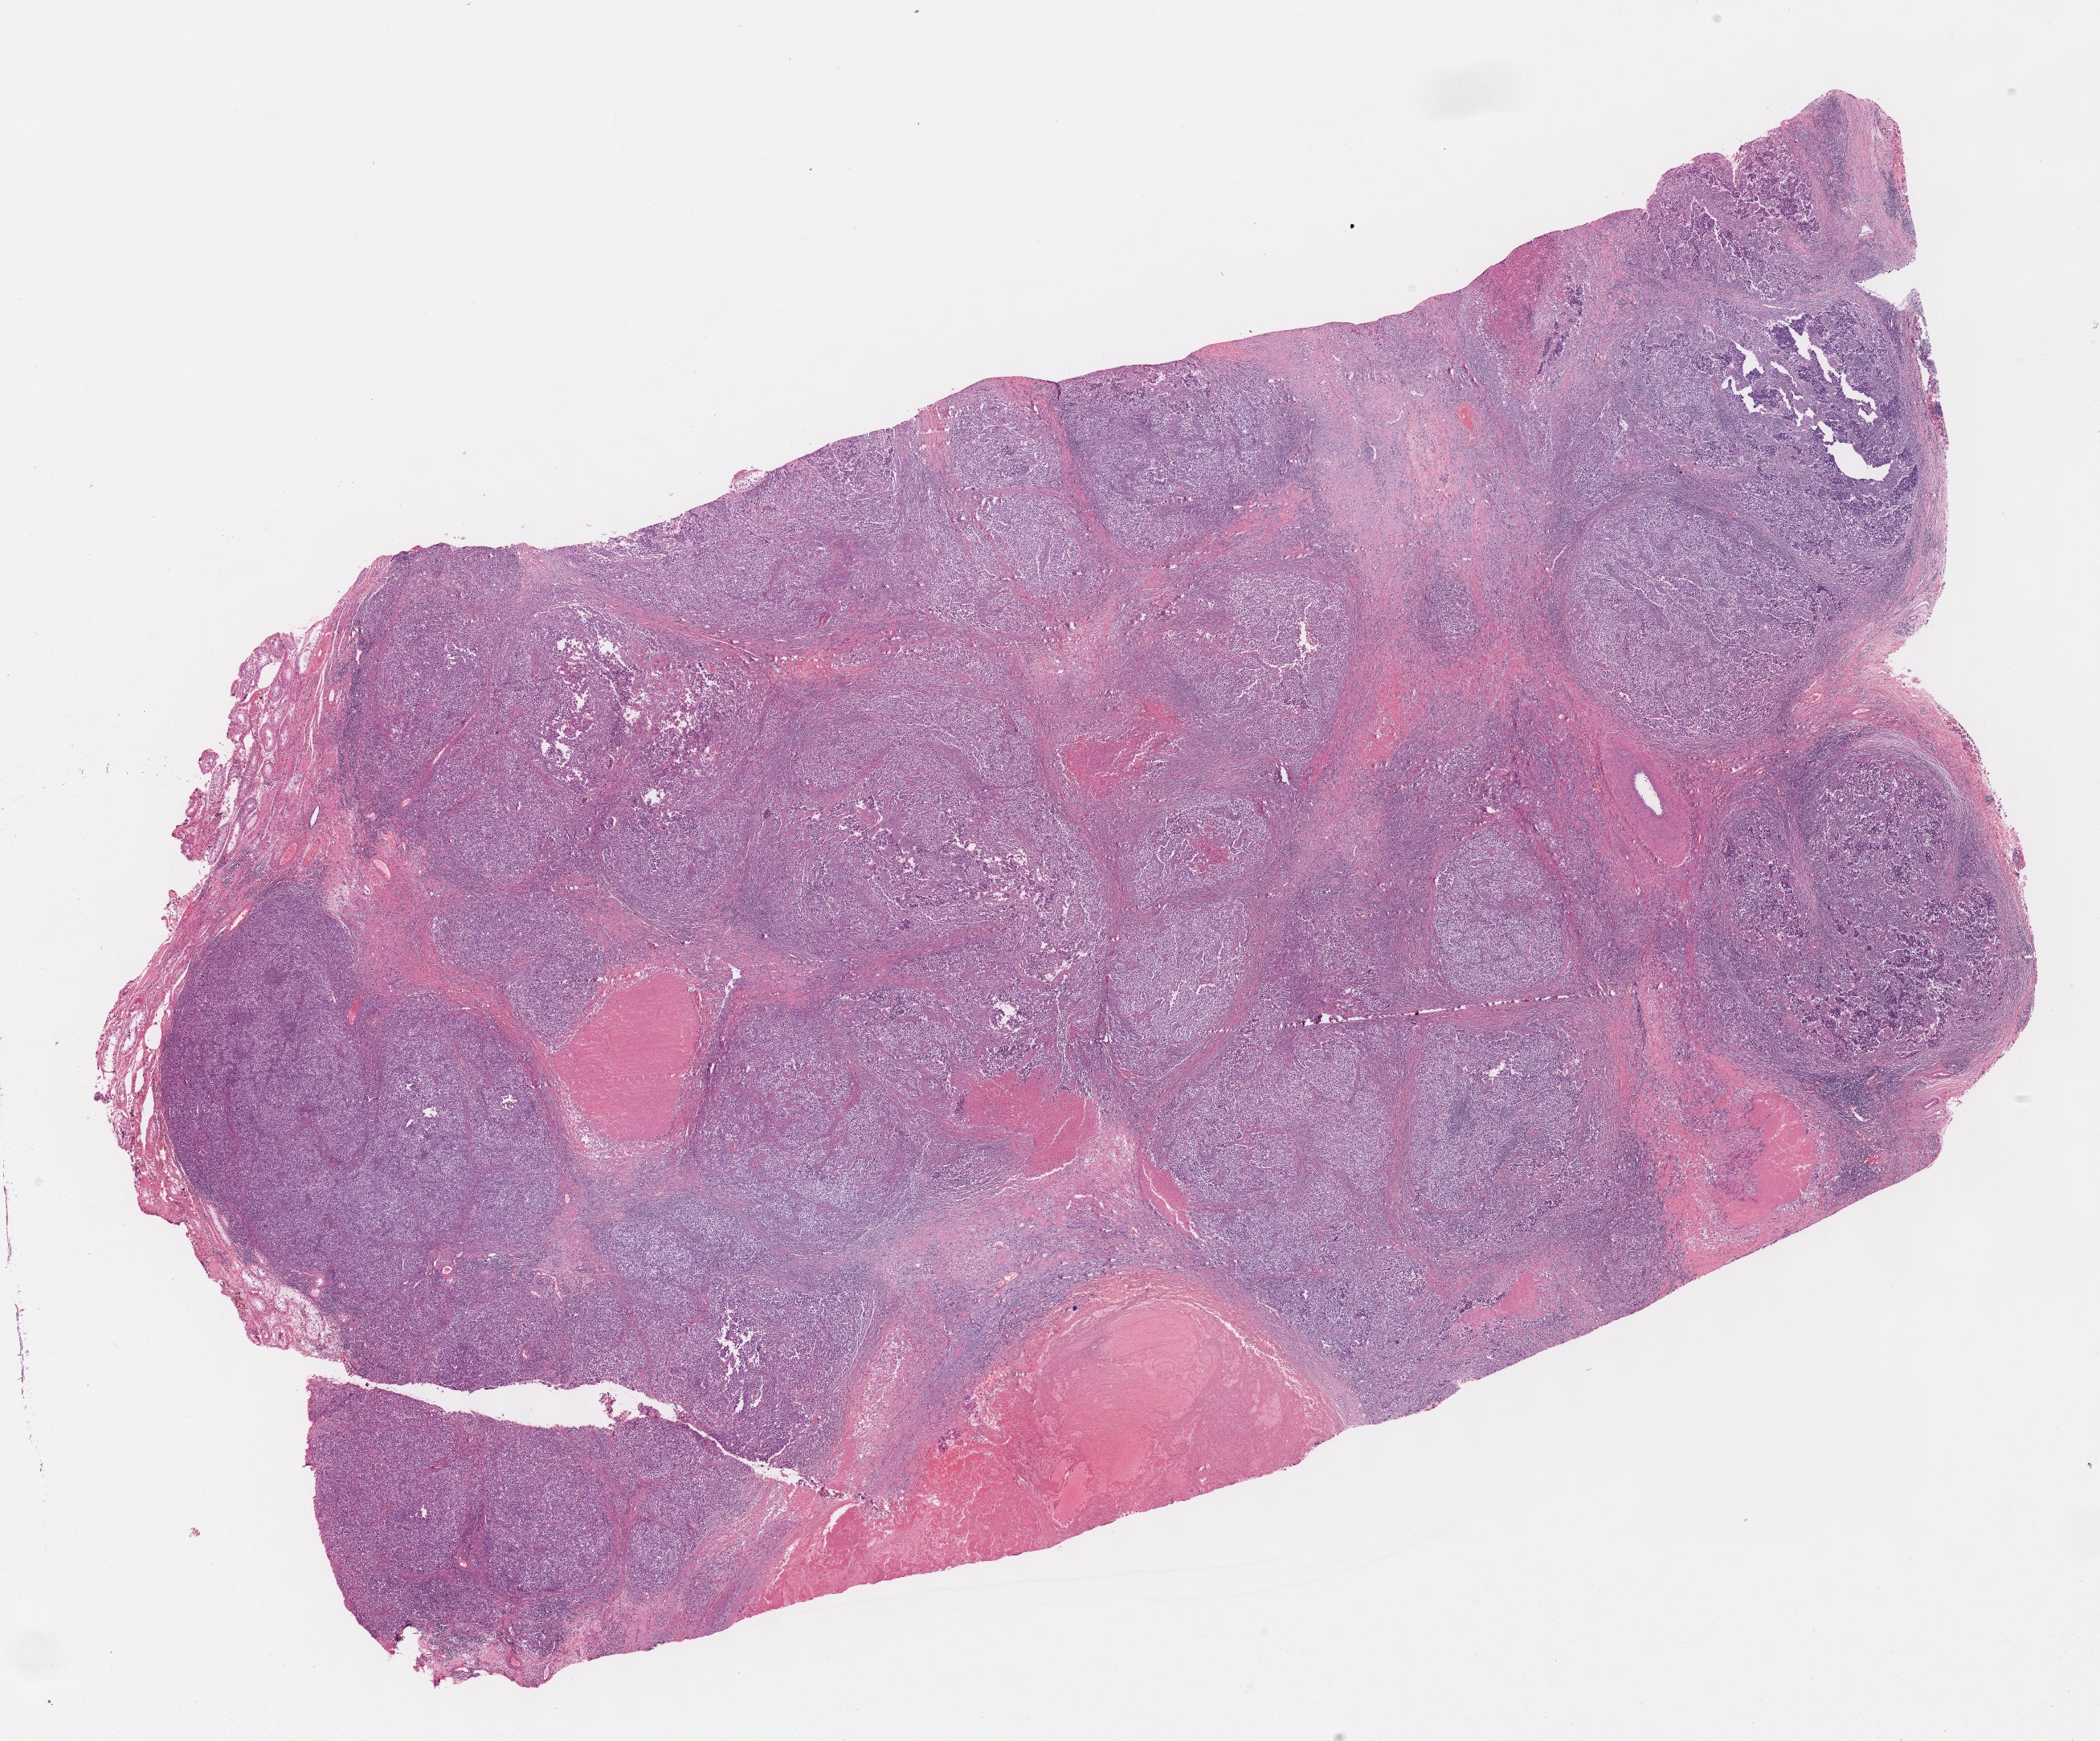
Digitized Hematoxylin and eosin (H&E) stained tissue section (whole slide) — shown as a low-resolution overview of the whole scanned area (about 21.1 x 17.5 mm, slide scanned at 40x); formalin-fixed paraffin-embedded (FFPE) diagnostic section; sample: primary tumour, testis. Patient: male, age at initial diagnosis 39 years.
AJCC pathologic stage: IB (6th edition). Pathologic diagnosis: Mixed germ cell tumor. TNM: T2 NX M0. Laterality: right.